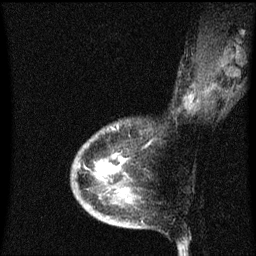
Breast MRI (dynamic contrast-enhanced), one sagittal slice. Slice 24 of 60 in the series (ordered by position). Dynamic contrast-enhanced series, image 2 of 3 at this slice position (ordered by acquisition). 1.5 T. TE 4.2 ms, TR 8.4 ms. 256 × 256 image matrix, field of view 200 × 200 mm. Female patient, age 38 years. From the clinical record (not read from this slice): setting: breast cancer imaged before/during neoadjuvant chemotherapy; receptor status: HR-positive, HER2-negative.
Structures marked on this image (semi-automatically segmented with operator editing):
- analysis volume of interest (the breast-tissue region the enhancement analysis was run in; not a lesion): bounding box [x1, y1, x2, y2] px = [72, 124, 135, 205]
- tumour enhancement mask (voxels above the 70 % enhancement threshold inside the analysis volume of interest): [98, 158, 125, 193]